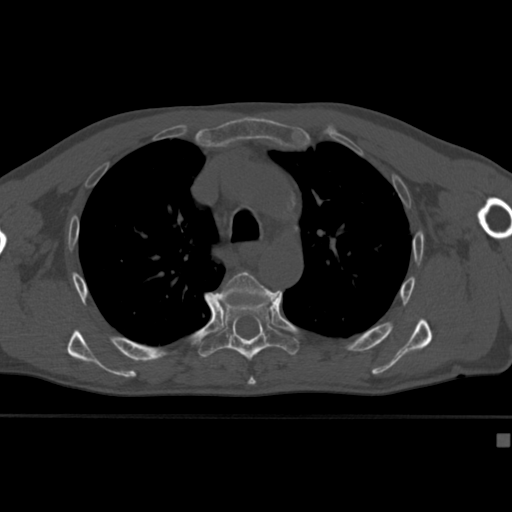
CT including the spine, one axial slice; reconstruction kernel Br40s; 120 kVp; bone window (W 1800 / L 400 HU); 512 × 512 image matrix, field of view 337 × 337 mm. Male patient, age 64 years. Case-level facts recorded for this patient, not image findings: primary cancer: uterus.
Outlined on this slice (semi-automatically segmented with operator editing):
- T5 vertebra: box from (x=214, y=271) to (x=281, y=382) px
- T6 vertebra: (x=198, y=301)–(x=299, y=361)